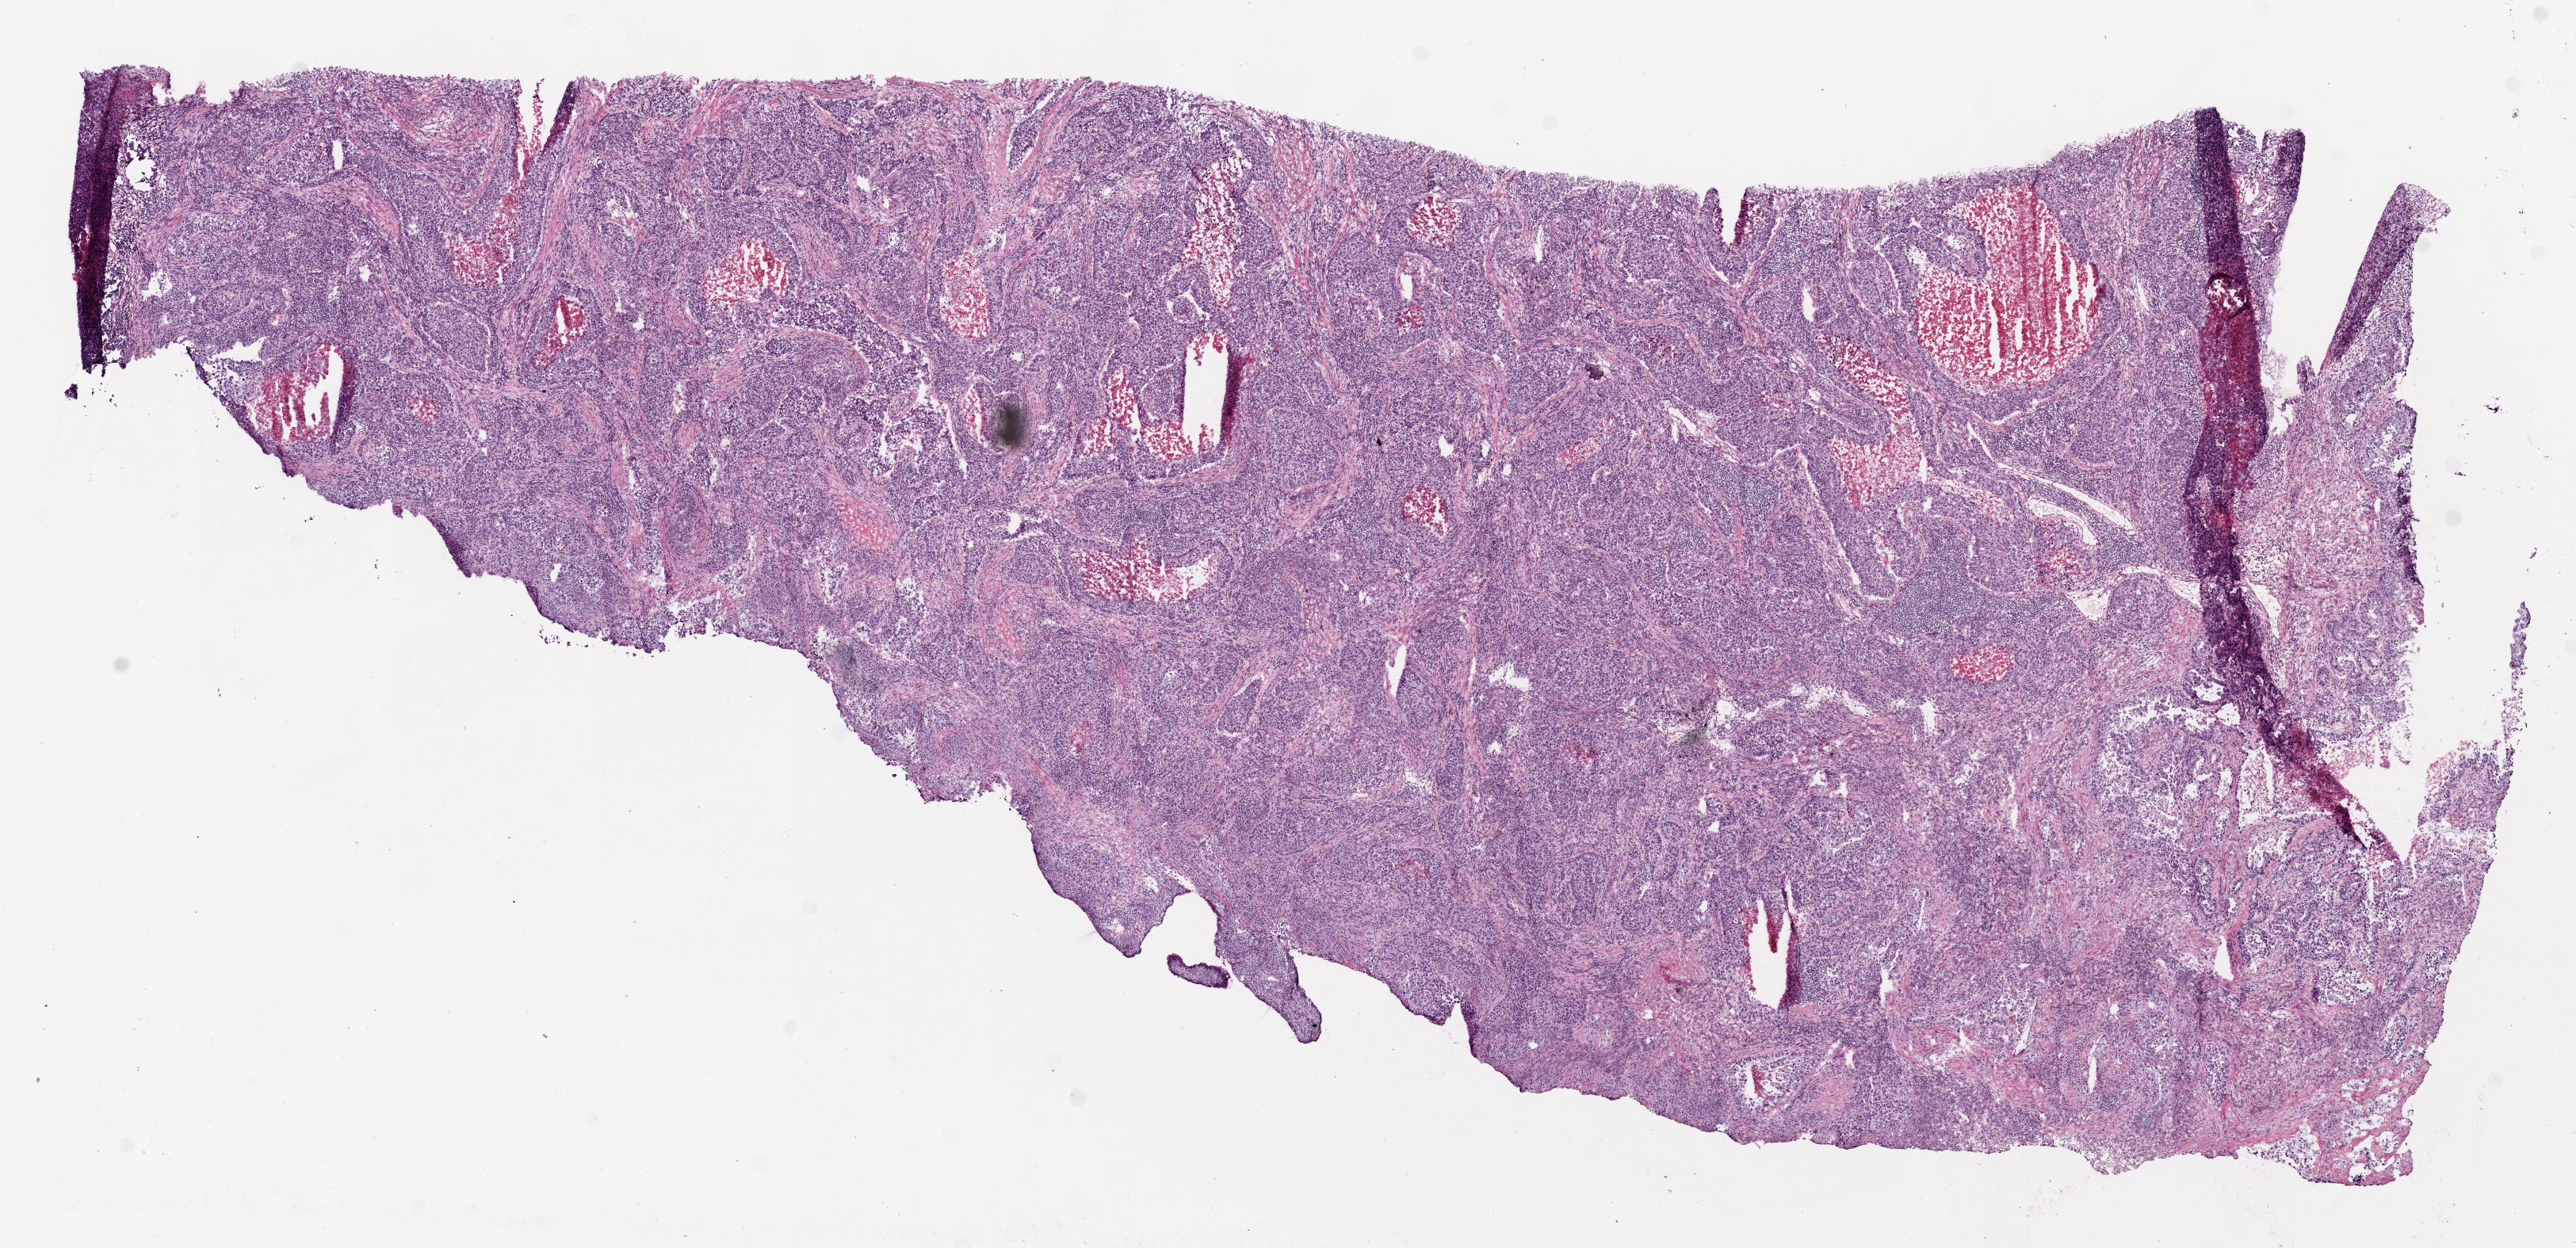
H&E whole-slide image — low-resolution overview of the scanned area, about 13.0 x 6.3 mm (from a 20x scan); frozen section from the bottom of the tissue portion; sample: primary tumour, lung. Patient: female, age at initial diagnosis 60 years. Slide review estimates, as recorded: tumour cells 60%, tumour nuclei 70%, normal cells 0%, stromal cells 20%, necrosis 20%.
TNM: T3 N2 M0. AJCC pathologic stage: IIIA. Histologic diagnosis: Squamous cell carcinoma, NOS (upper lobe, lung).